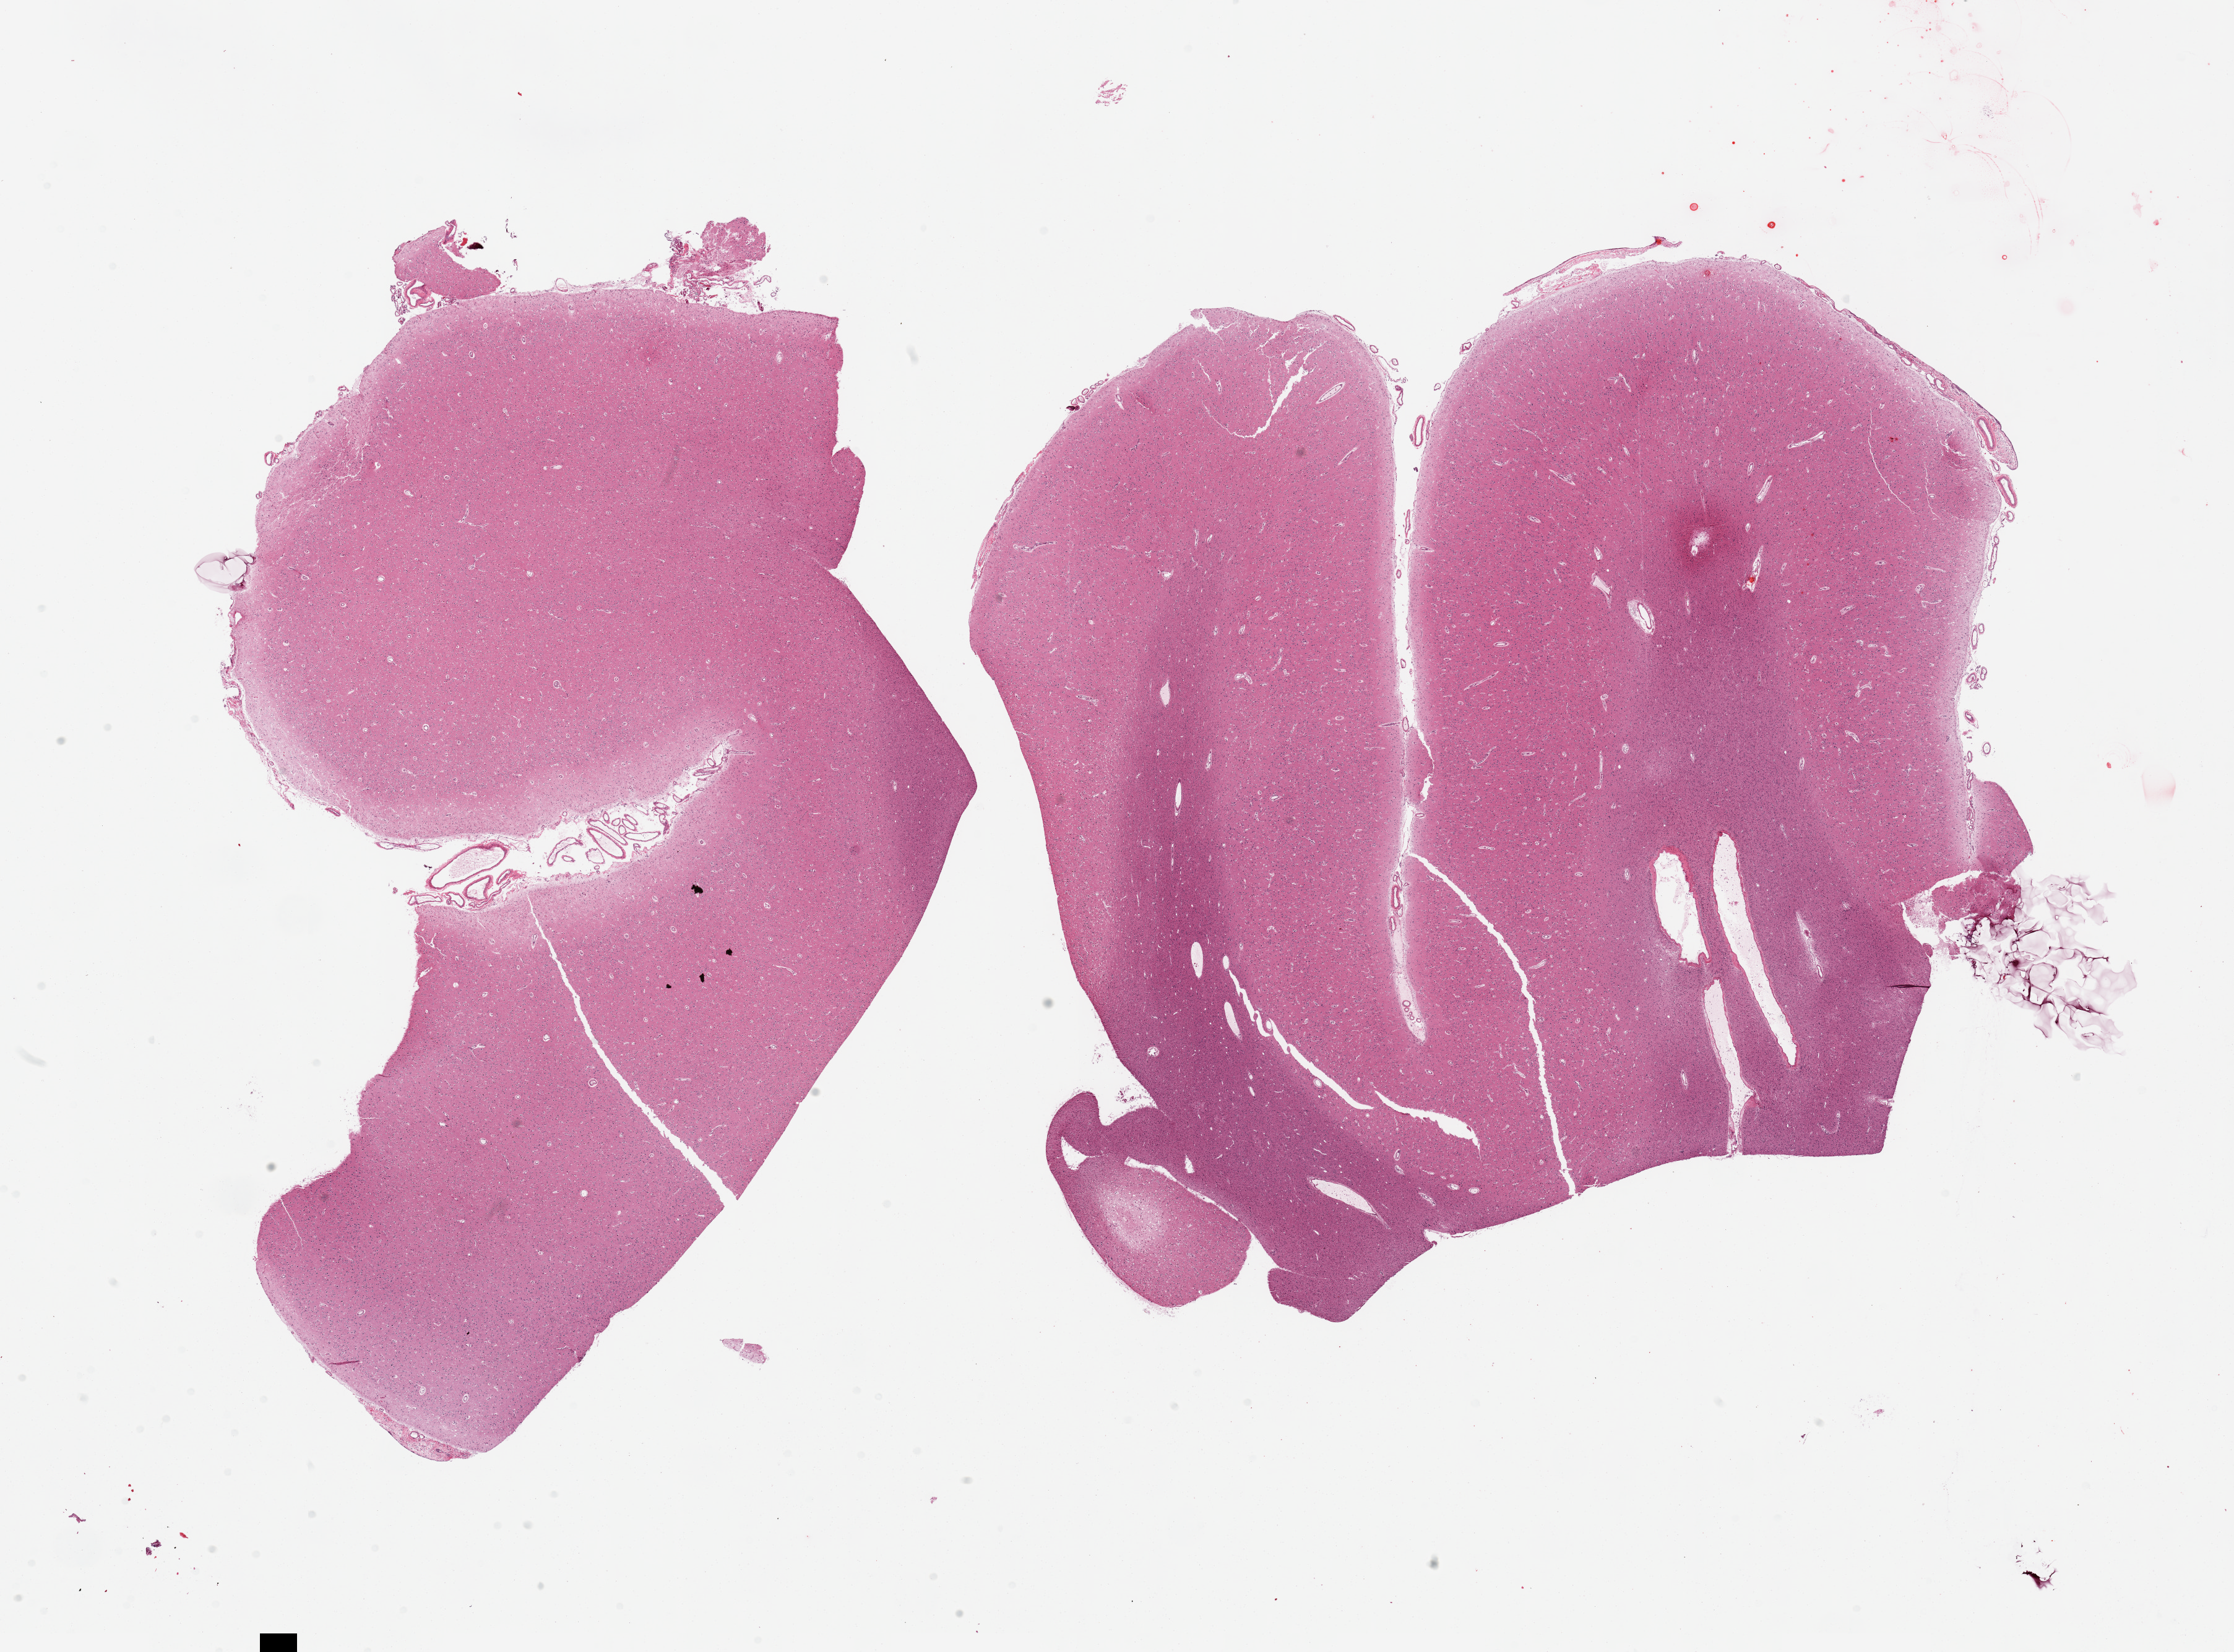
Whole-slide image, haematoxylin and eosin stain — a low-resolution overview of the entire scanned area, about 28.5 x 21.1 mm; PAXgene-fixed paraffin-embedded (PFPE) section; target tissue: cerebral cortex; tissue donor sample. Donor: male.
• reviewer comment on this tissue sample: 2 pieces, no abnormalities